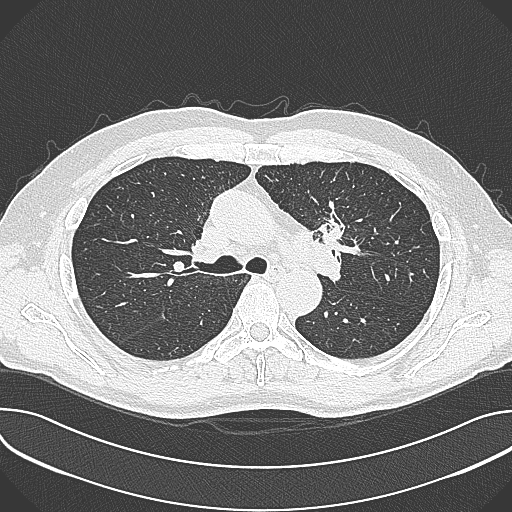
Low-dose screening chest CT, axial slice; baseline annual screen; lung window (W 1500 / L -600 HU); 1 mm slice thickness; lung (sharp) reconstruction kernel (B80f); 120 kVp. Male participant, aged 59 years at enrolment. Current smoker at enrolment.
- Lesion marked by an expert reader, bounding box (x1, y1, x2, y2) in pixels: (303, 193, 365, 256).
- The screening reader recorded 2 non-calcified nodules or masses ≥4 mm on this exam (left upper lobe, left upper lobe); which of them this box marks is not recorded.
- Official screen result: positive, change unspecified: nodule(s) >= 4 mm or enlarging nodule(s), mass(es), or other non-specific abnormalities suspicious for lung cancer.
- Later outcome: lung cancer diagnosed 21 days after this screen — non-small cell carcinoma, left upper lobe, poorly differentiated (G3), stage IIIA (AJCC 6th edition), 35 mm at pathology.